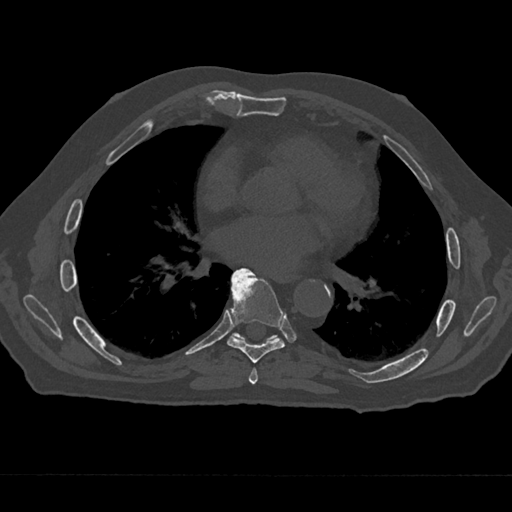
CT including the spine, one axial slice; position 360 of 797 along the scan axis; bone window (W 1800 / L 400 HU); 0.5 mm slice thickness; 512 × 512 image matrix. Male patient, age 75 years. From the clinical record (not read from this slice): primary cancer: renal; vertebrae with lytic lesions (as recorded): T4.
Structures marked on this image (semi-automatically segmented with operator editing):
- T6 vertebra: bounding box [x1, y1, x2, y2] px = [249, 368, 258, 385]
- T7 vertebra: [227, 268, 285, 363]
- T8 vertebra: [232, 333, 277, 341]